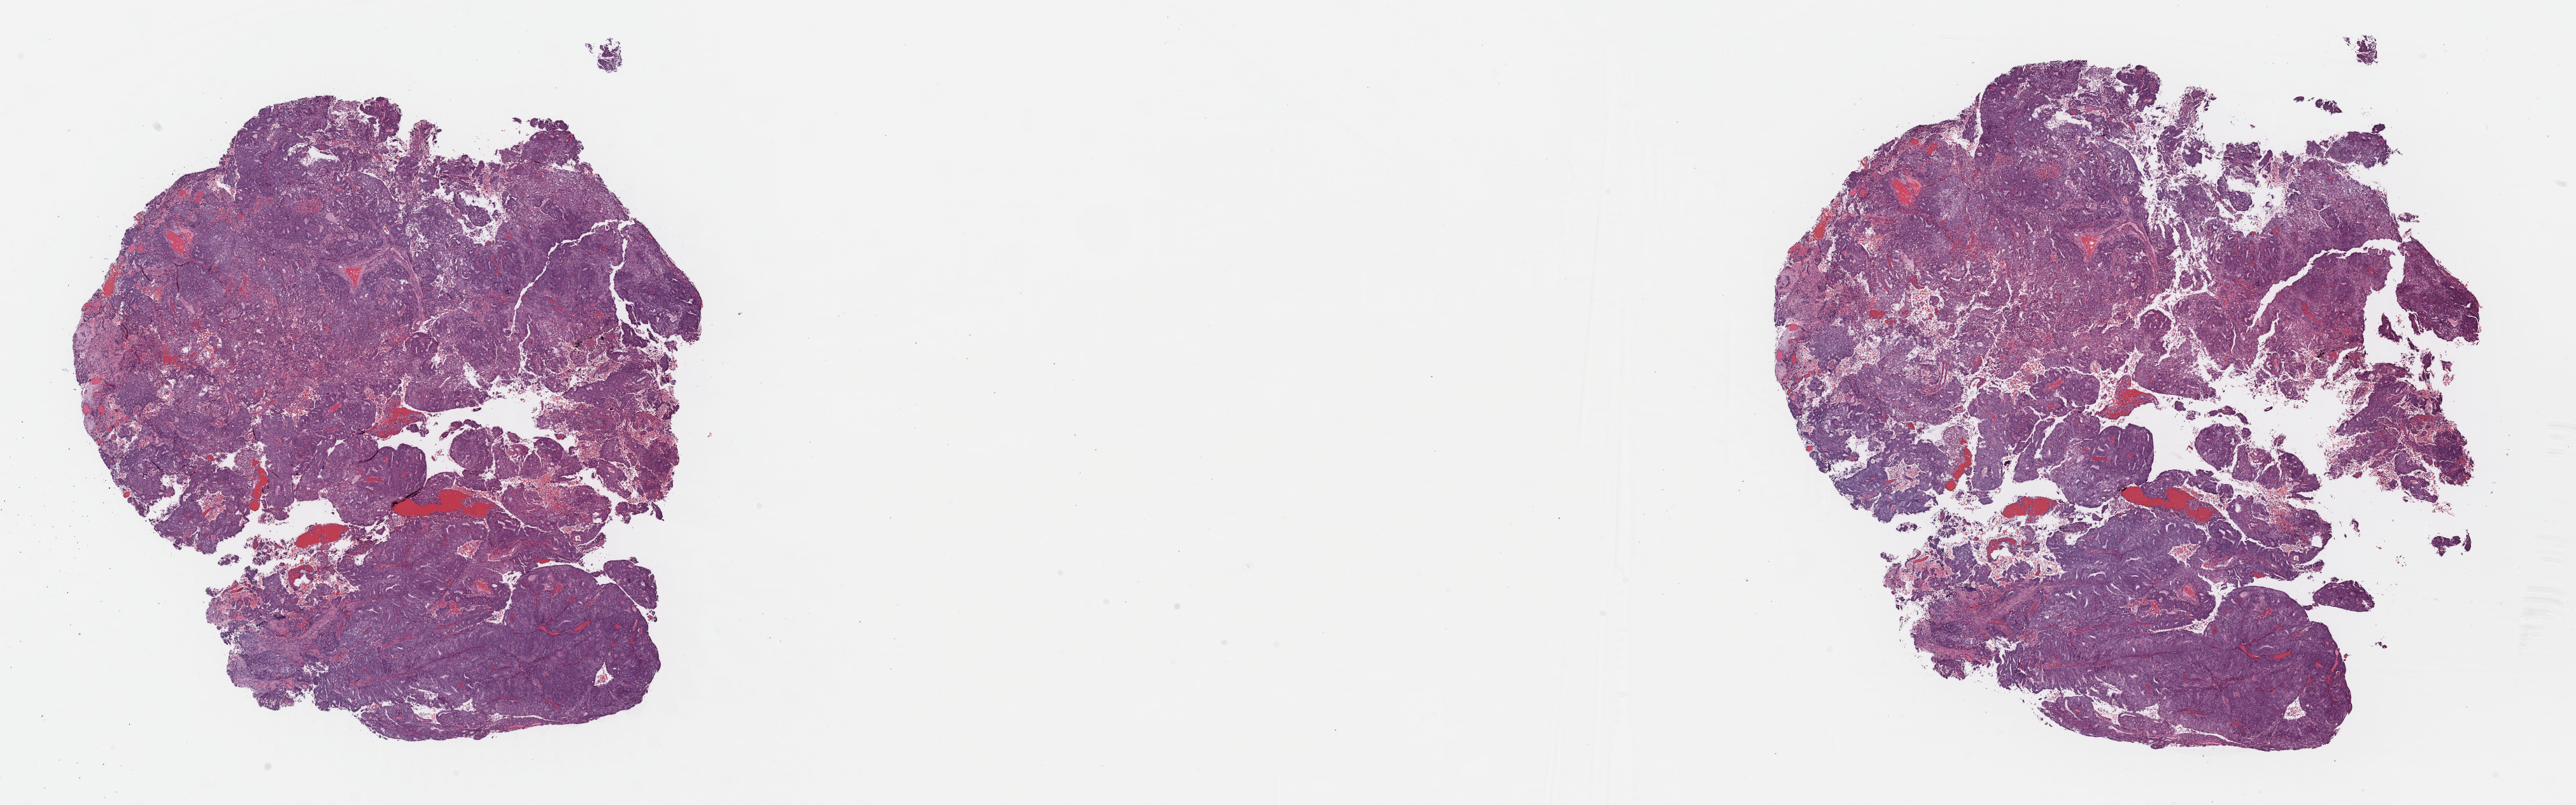
Whole-slide histology image, H&E, a low-resolution overview of the entire scanned area, about 31.9 x 10.0 mm (acquisition: 40x scan). Formalin-fixed paraffin-embedded (FFPE) diagnostic section. Sample: primary tumour, uterus. Female, age 58 years at initial diagnosis. Histologic grade: G3 (poorly differentiated).
FIGO stage: IB. Histologic diagnosis: Endometrioid adenocarcinoma, NOS (endometrium).